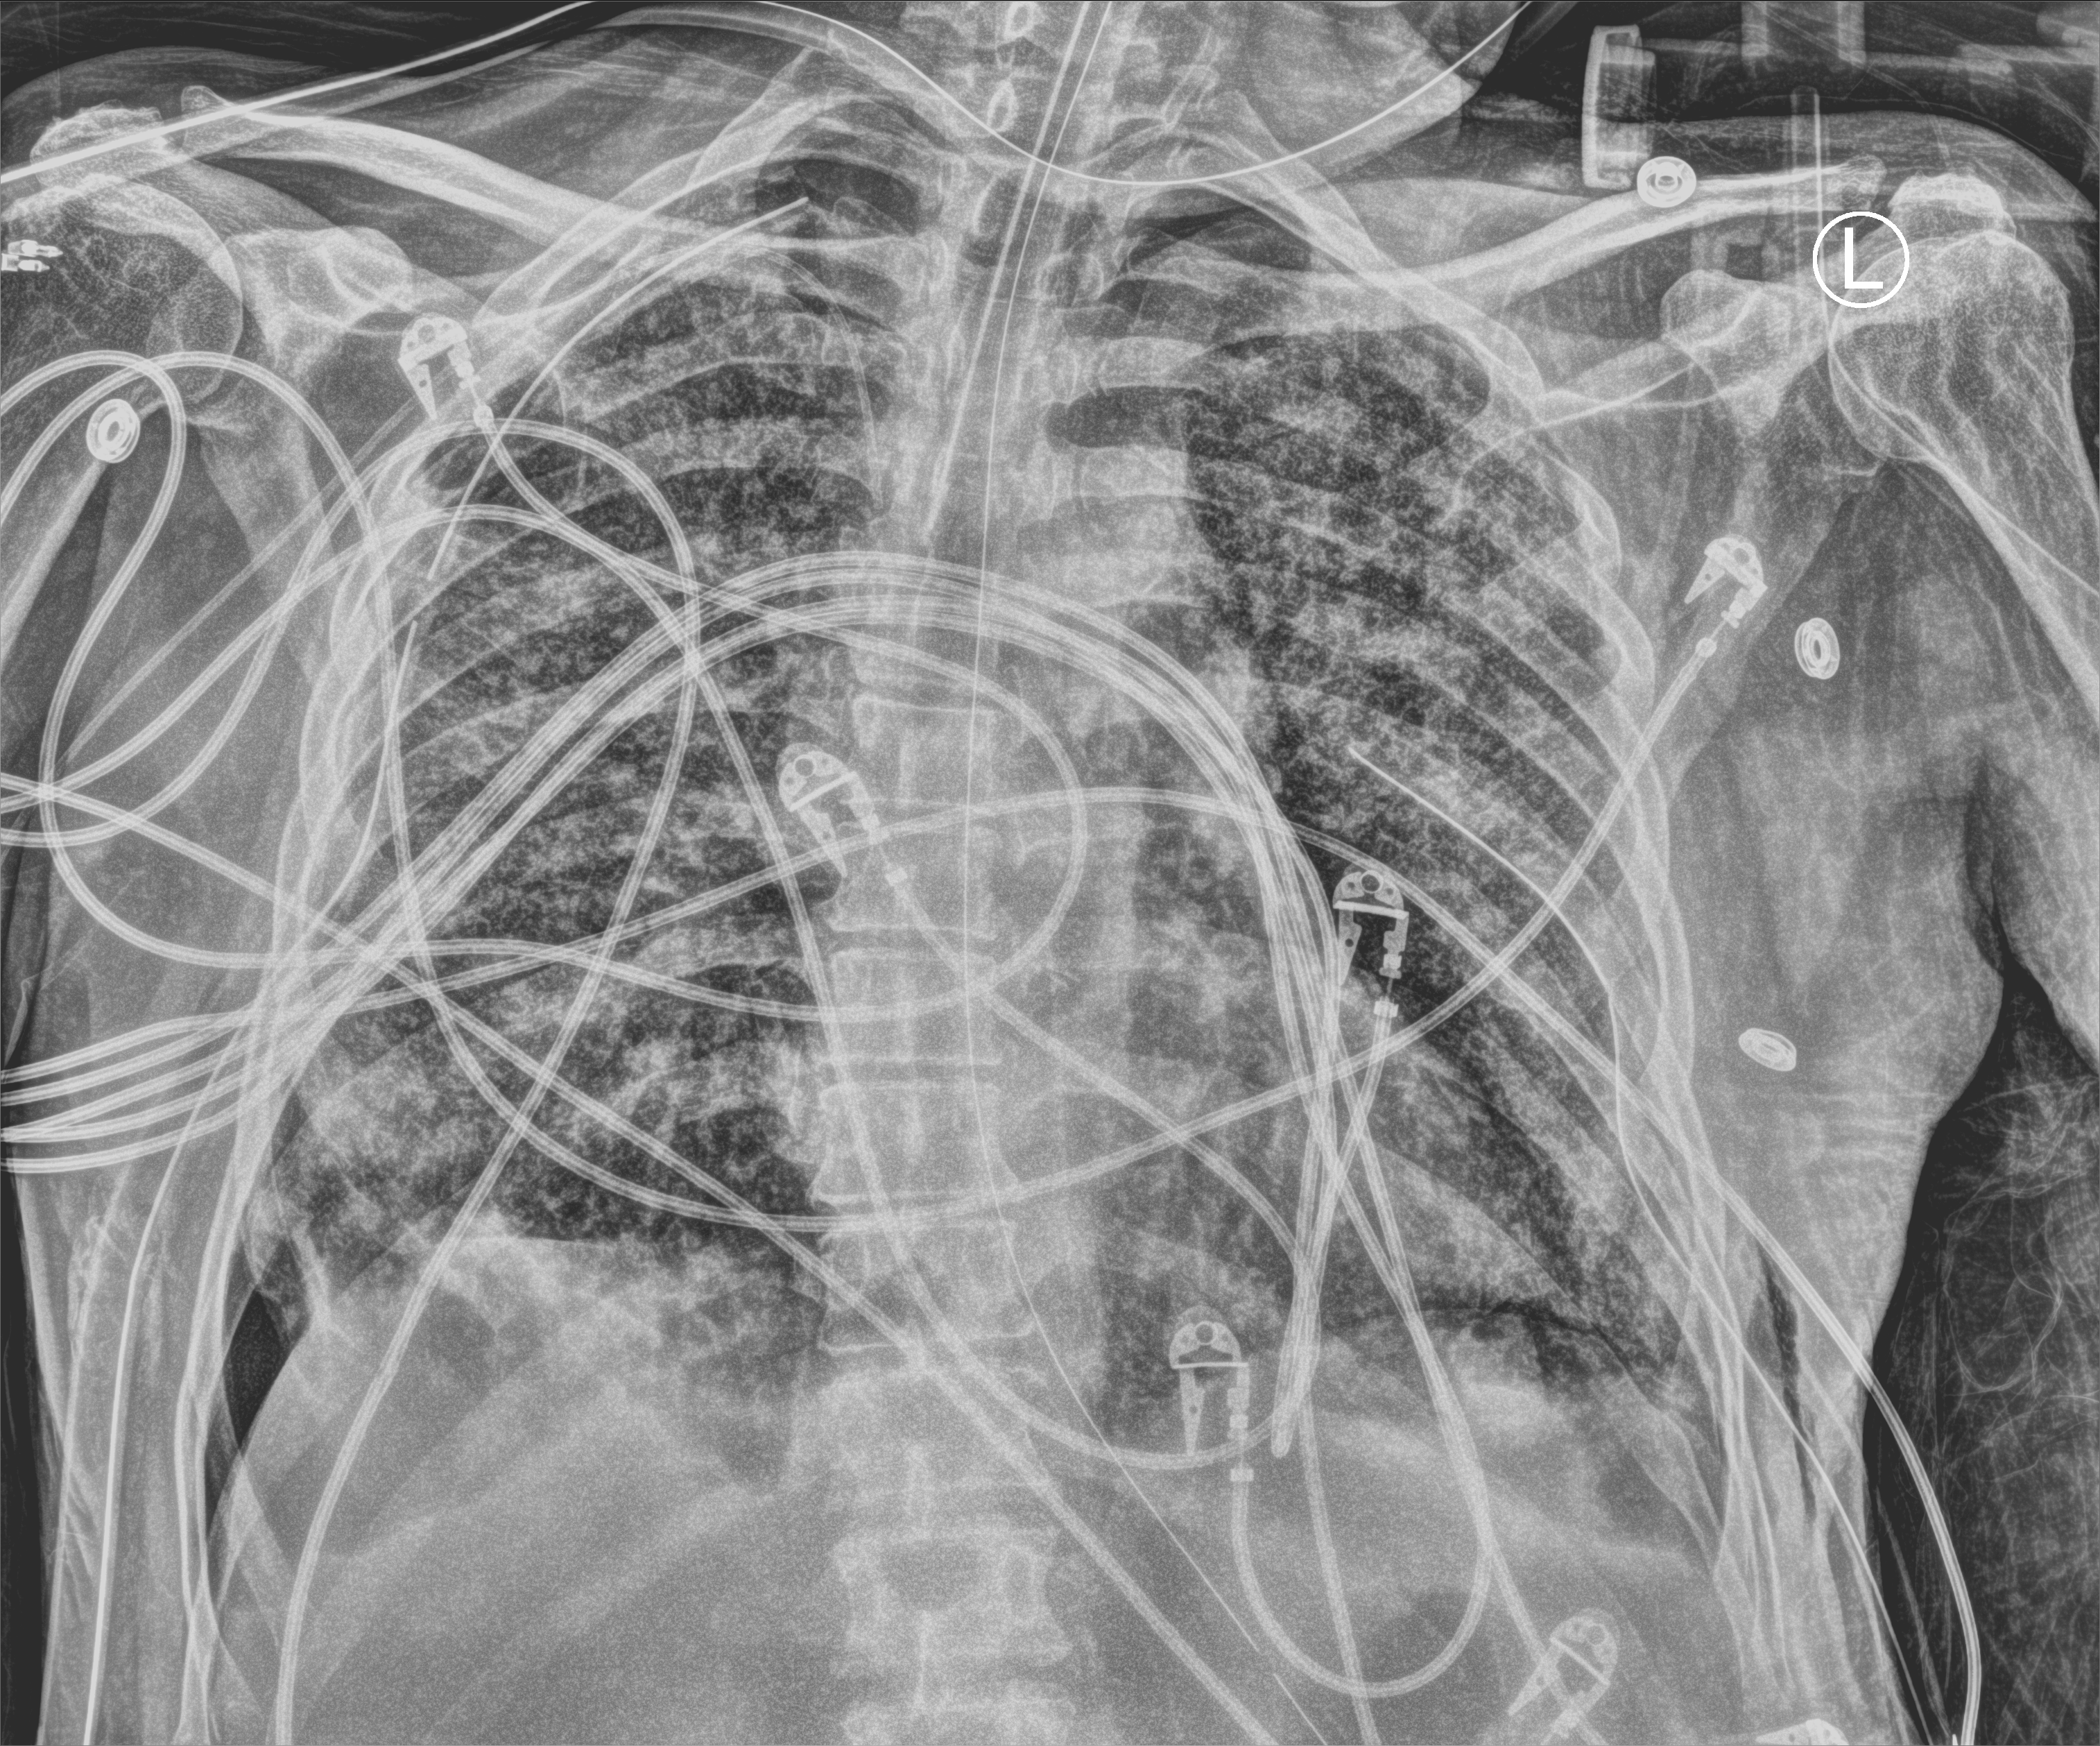
Chest X-ray (portable). Male patient hospitalised with COVID-19, age 60–74 years.
From the hospital-stay record, not from the radiograph (when in the stay this image was taken is not recorded): smoking status (admission record): never; mechanically ventilated during this hospital stay: yes.